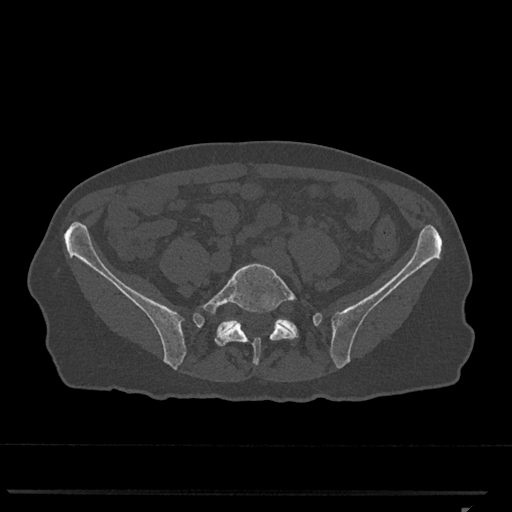
CT including the spine, one axial slice; position 140 of 793 along the scan axis; reconstruction kernel Br40s/3; bone window (W 1800 / L 400 HU); 512 × 512 image matrix, field of view 380 × 380 mm. Female patient, age 62 years. Case-level facts recorded for this patient, not image findings: primary cancer: renal.
Outlined on this slice (semi-automatically segmented with operator editing):
- L5 vertebra: bounding box (x1, y1, x2, y2) in pixels: (201, 263, 297, 365)